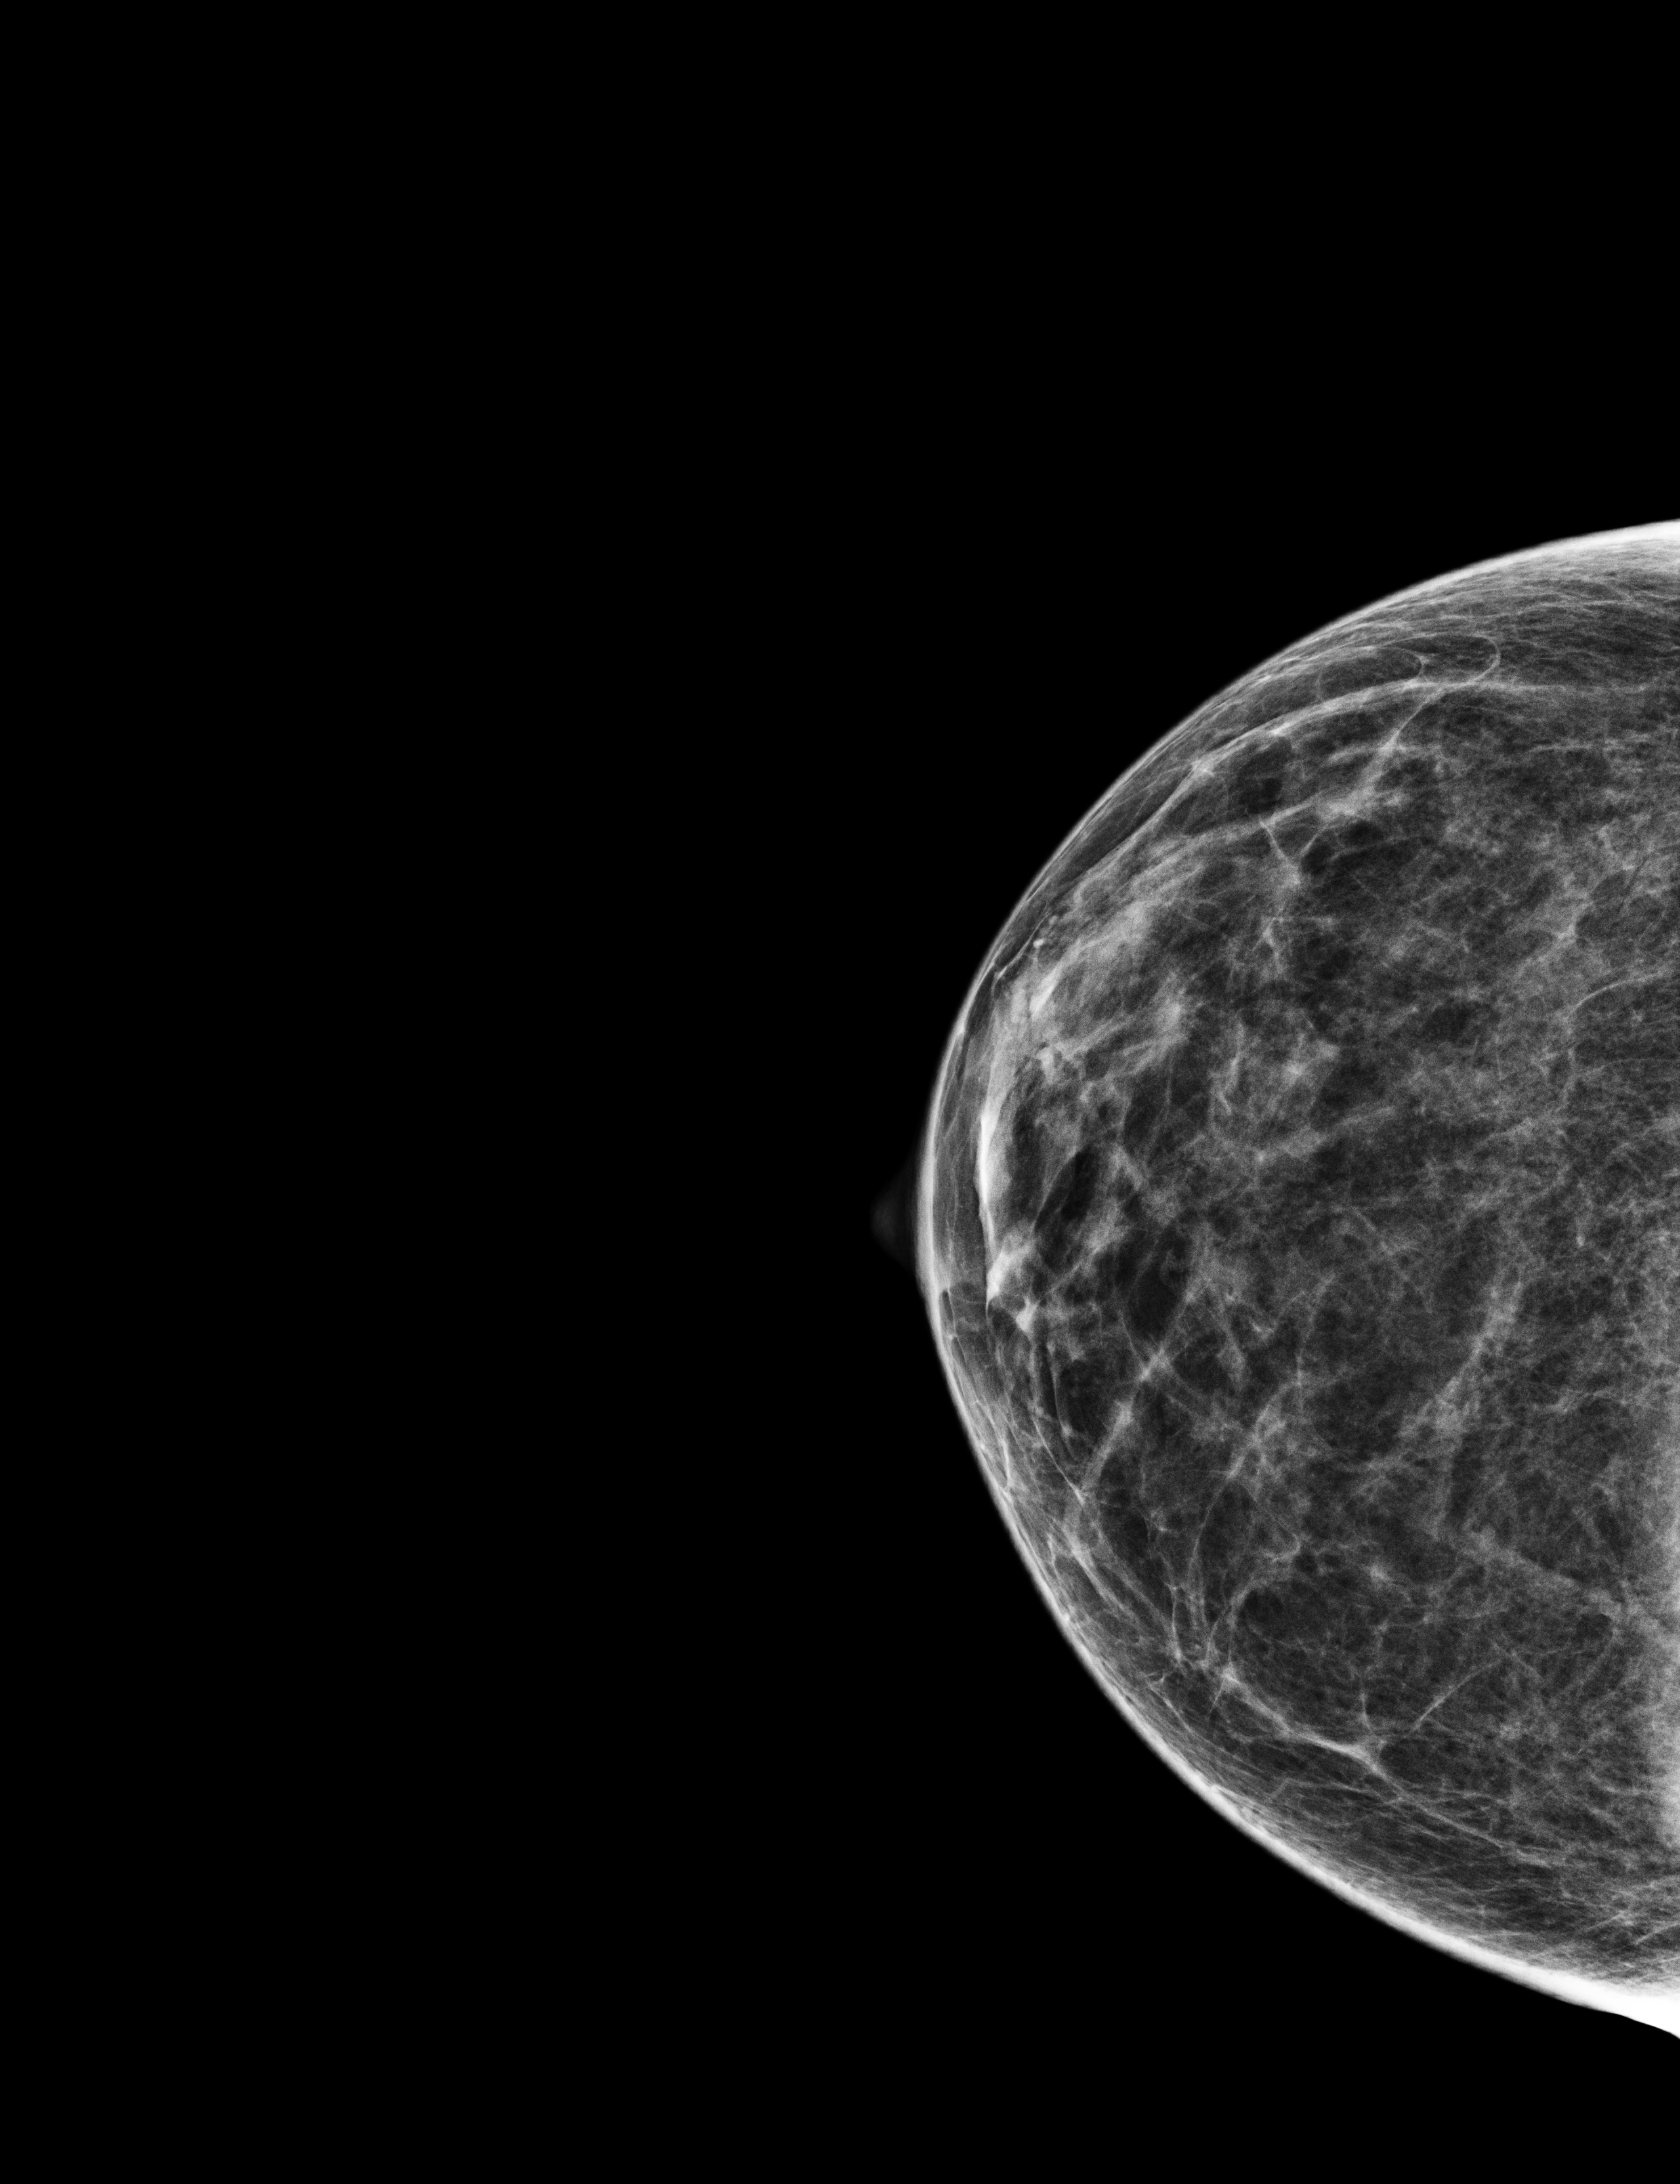
Screening examination; compressed breast thickness 38 mm; system: Selenia Dimensions.
Image type: full-field digital mammogram. Breast: right. Projection: craniocaudal (CC) view.